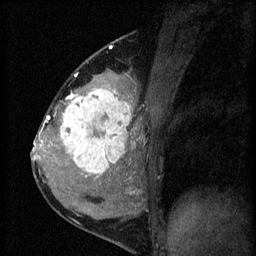
Breast MRI (dynamic contrast-enhanced), one sagittal slice. 3 images stored at this slice position (order not interpretable as contrast timing). 1.5 T. TE 4.2 ms, TR 8.2 ms. 2 mm slice thickness. 256 × 256 image matrix, field of view 180 × 180 mm. Female patient, age 37 years.
Outlined on this slice (semi-automatic segmentation, software-assisted and operator-edited):
- analysis volume of interest (the breast-tissue region the enhancement analysis was run in; not a lesion): bounding box (x1, y1, x2, y2) in pixels: (53, 78, 140, 181)
- tumour enhancement mask (voxels above the 70 % enhancement threshold inside the analysis volume of interest): (54, 90, 137, 177)